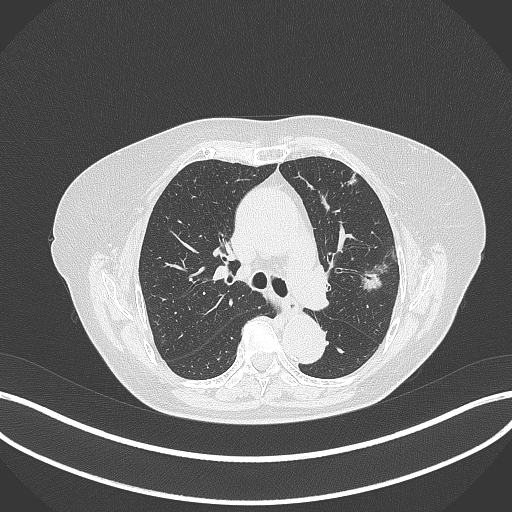
Chest CT, one axial slice; position 213 of 316 along the scan axis; reconstruction kernel B70f; lung window (W 1500 / L -600 HU); 1 mm slice thickness; 512 × 512 image matrix. Patient: female, 75 years. Case-level facts recorded for this patient, not image findings: clinical TNM (as recorded): T1c N0 M0.
Annotated regions visible in this slice (bounding box drawn by a radiologist):
- lung tumour (recorded histology: adenocarcinoma): bounding box <359,271,384,296> (left, top, right, bottom; pixels)